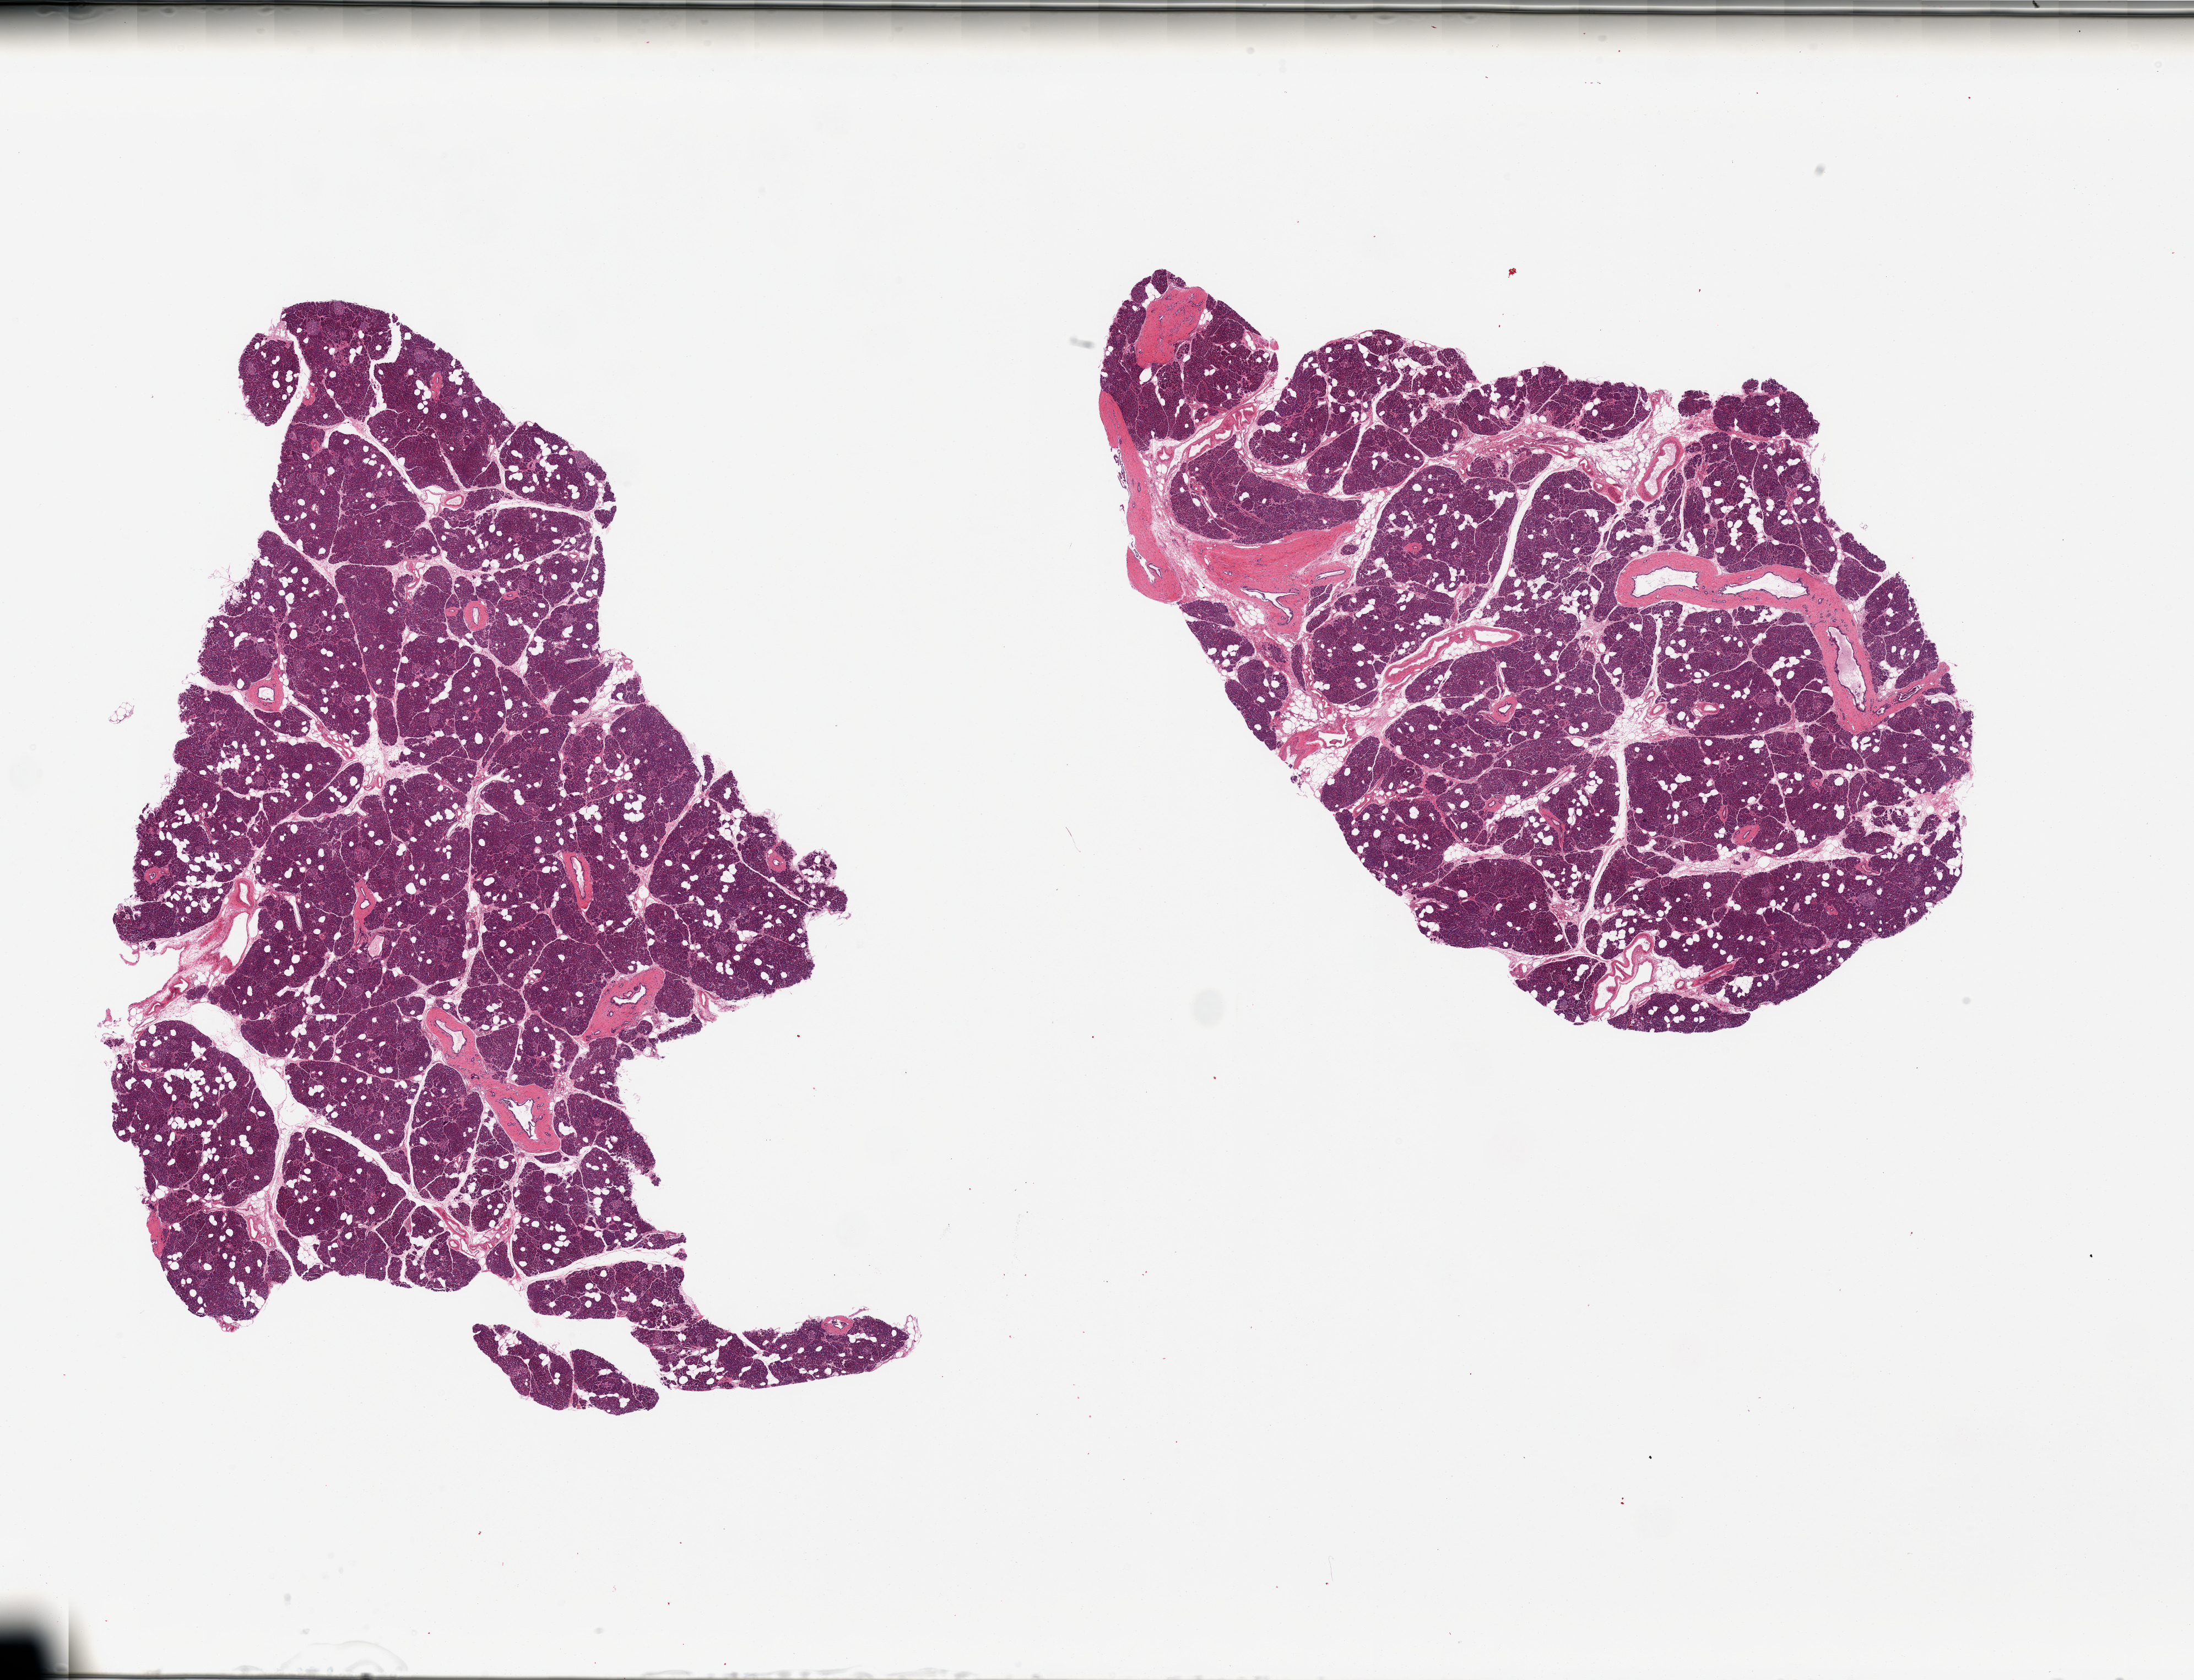
Digitized haematoxylin and eosin-stained section, brightfield, a low-resolution overview of the entire scanned area, about 31.5 x 24.1 mm (acquisition: 20x scan). PAXgene-fixed paraffin-embedded (PFPE) section. Section of pancreas (target tissue). Tissue donor sample. Donor: female.
Review note (as recorded): 2 pieces; 10% individual fat cells diffusely distributed amonst parenchyma.